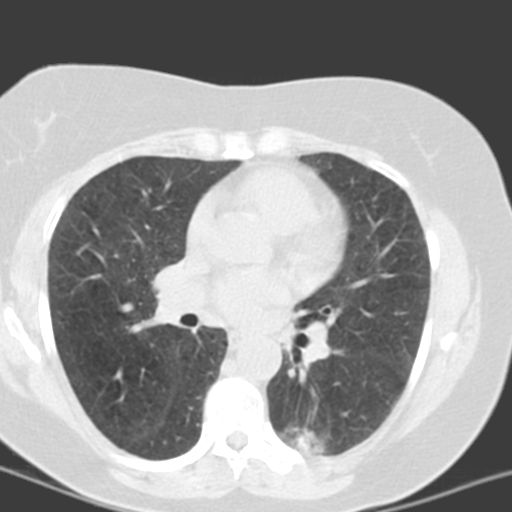
Low-dose screening chest CT, one axial slice; slice 87 of 150 in the series (ordered by position); 120 kVp; lung window (W 1500 / L -600 HU); 3.2 mm slice thickness; 512 × 512 image matrix, field of view 290 × 290 mm.
Annotated regions visible in this slice (expert manual segmentation):
- lesion 2 (tumor, lower lobe of left lung): bounding box [x1, y1, x2, y2] px = [295, 430, 321, 453]